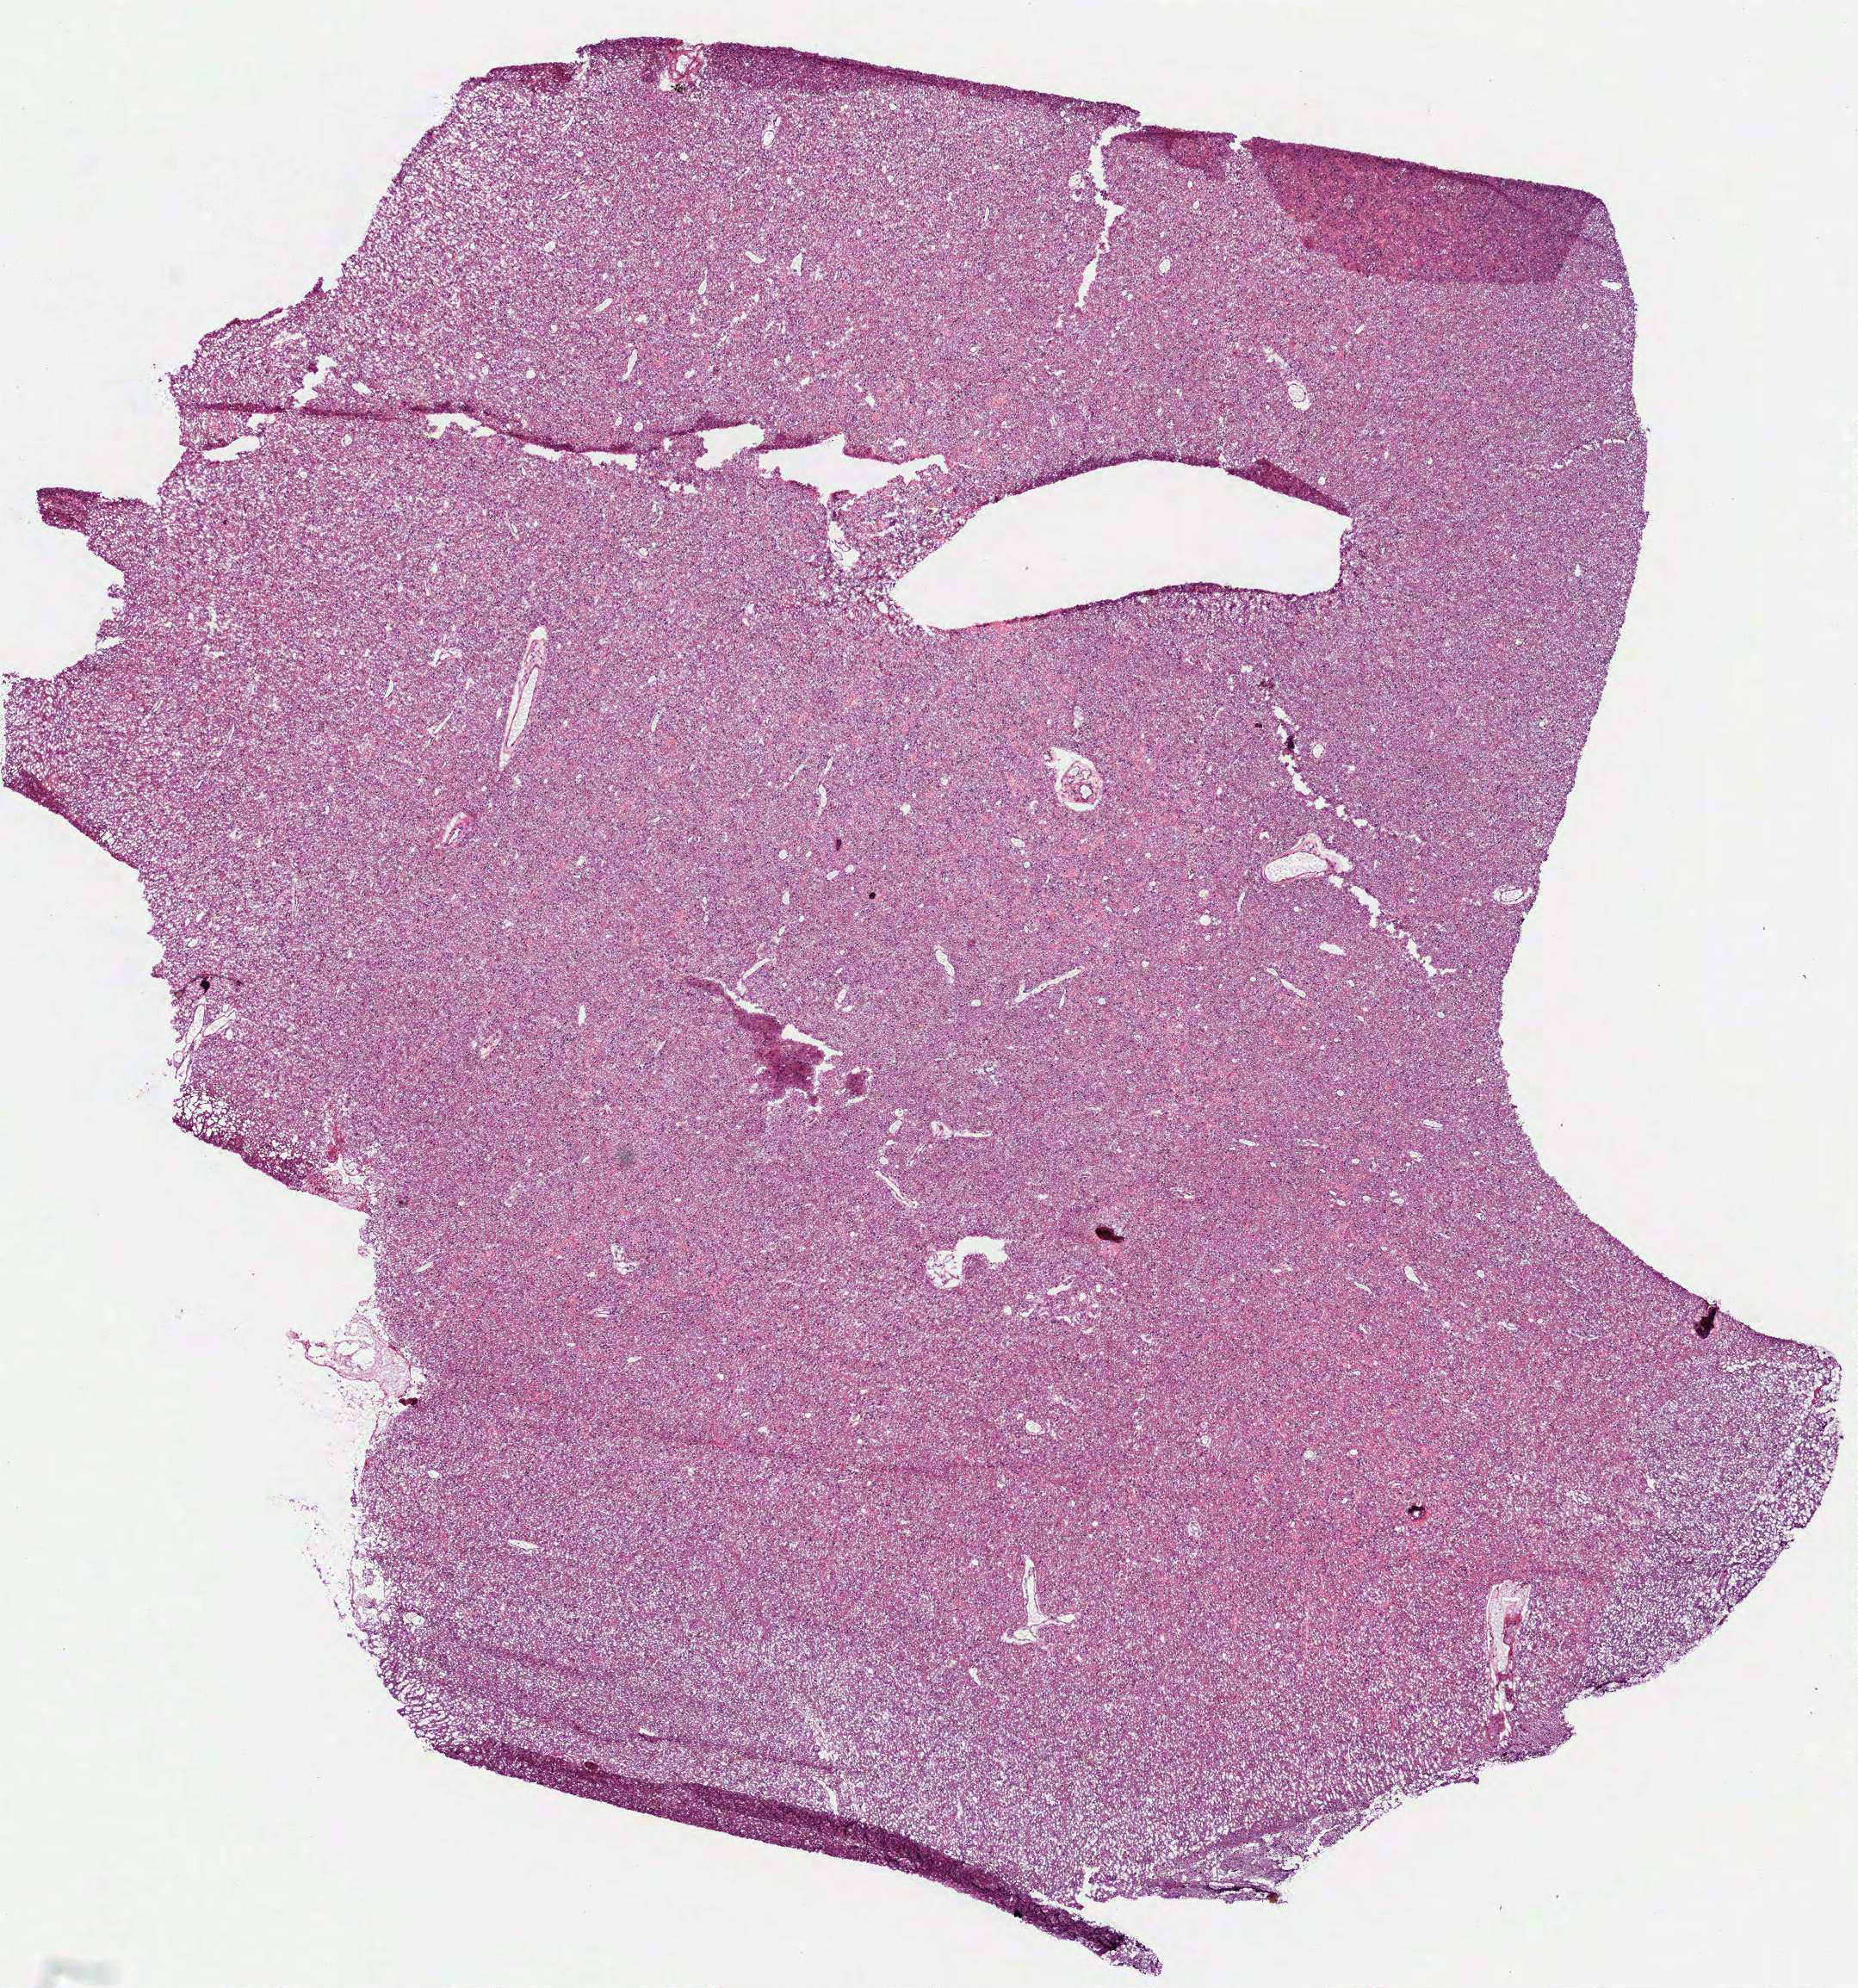
Digitized H&E tissue section (whole slide), whole scanned area (about 8.7 x 9.3 mm, acquisition: 40x scan) shown as a low-resolution overview. Frozen section from the bottom of the tissue portion. Sample: primary tumour, brain. Male, age 39 years at initial diagnosis. Histologic grade: G2 (moderately differentiated). Slide review estimates, as recorded: tumour cells 100%, tumour nuclei 65%, normal cells 0%, stromal cells 0%, necrosis 0%.
Histologic diagnosis: Oligodendroglioma, NOS.